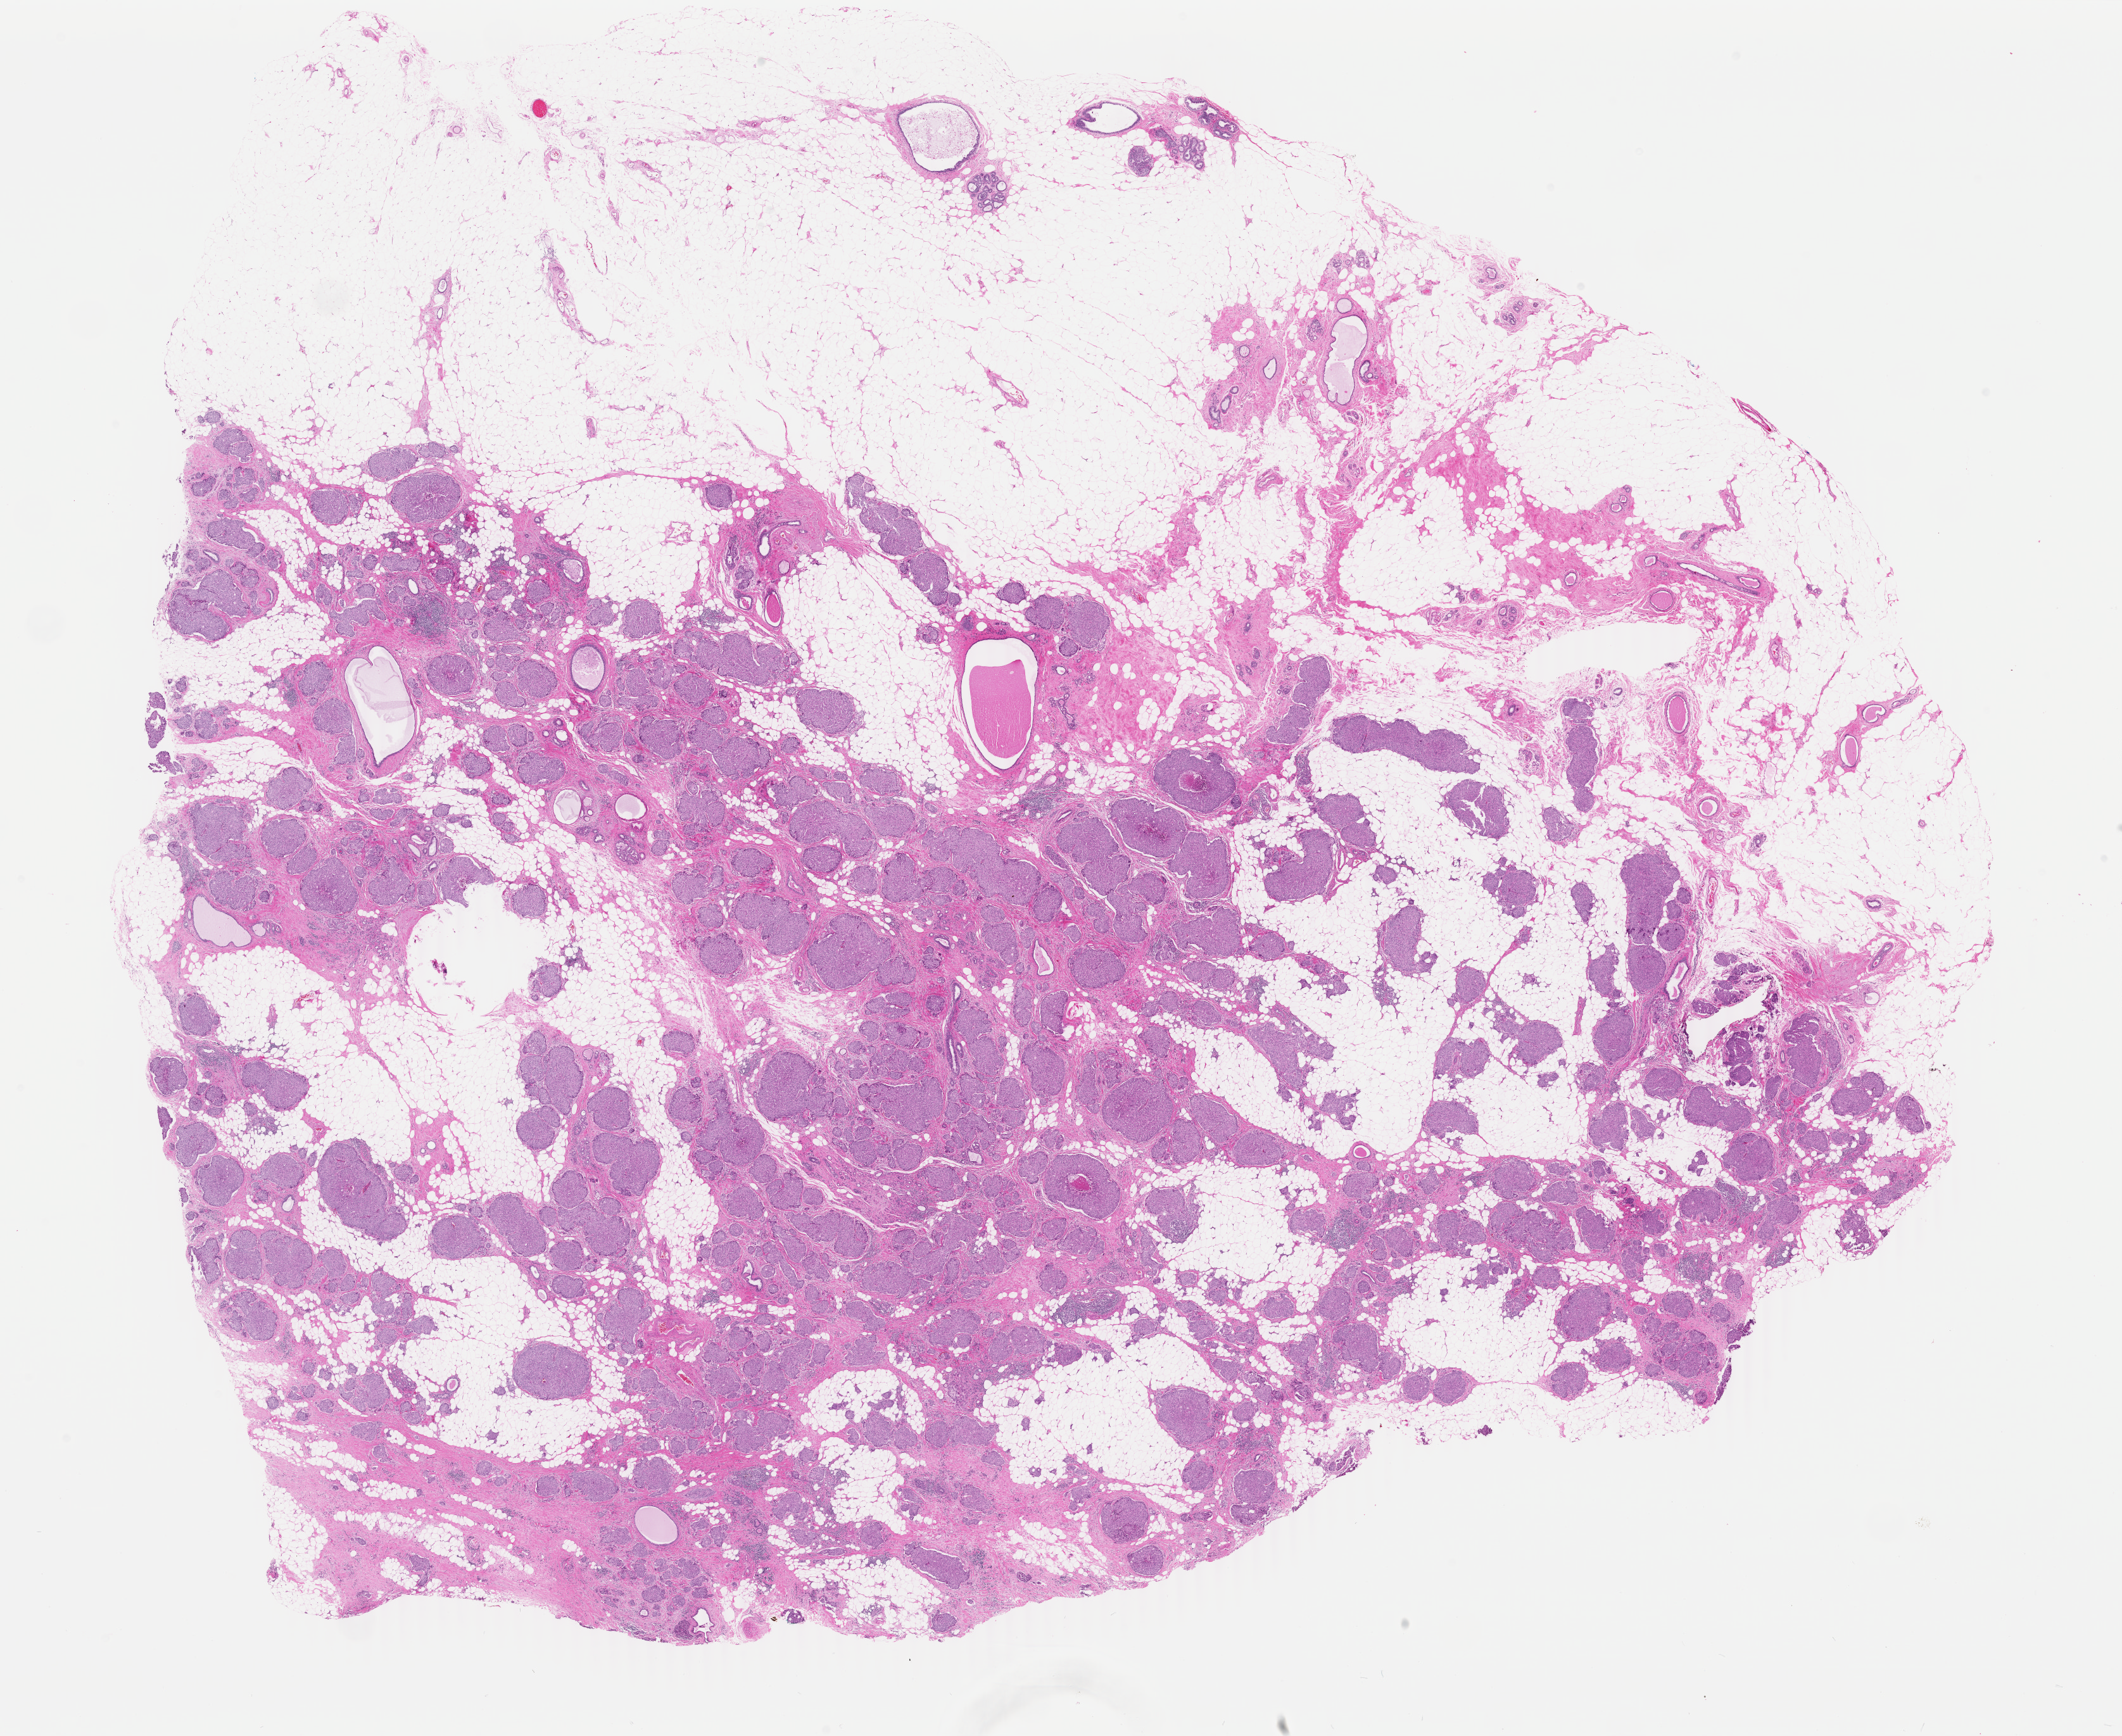
Whole-slide histology image, H&E-stained, low-resolution overview of the scanned area, about 26.7 x 21.8 mm, FFPE section, primary tumour sample from the breast. Female, age 71 years at initial diagnosis.
Lymph nodes positive (case pathology): 2 of 15 examined. Laterality: right. AJCC pathologic stage: IIIA (7th edition). Histologic diagnosis: Infiltrating duct carcinoma, NOS.